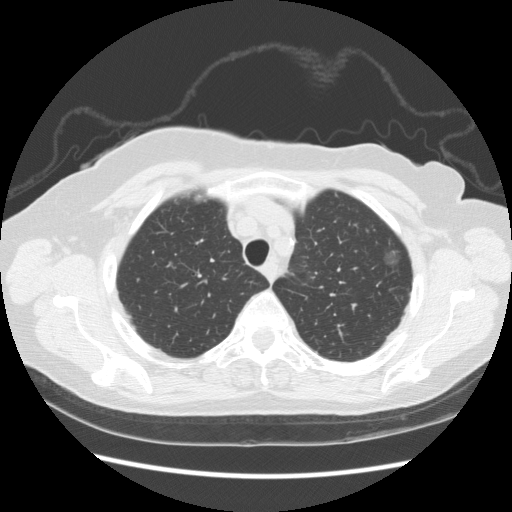
Axial slice from a low-dose chest CT screening exam. Baseline annual screen. Lung window (W 1500 / L -600 HU). 2.5 mm slice thickness. Slice 36 of 247 in the series. 512 × 512 image matrix. Female participant, aged 73 years at enrolment. Former smoker at enrolment.
Expert-annotated lung lesion, box from (x=373, y=230) to (x=415, y=276) px. The screening reader recorded 3 non-calcified nodules or masses ≥4 mm on this exam (left upper lobe, left upper lobe, left upper lobe); which of them this box marks is not recorded. Participant outcome: lung cancer diagnosed 445 days after this screen — bronchiolo-alveolar adenocarcinoma, NOS, left upper lobe, well differentiated (G1), stage IA (AJCC 6th edition), 10 mm at pathology.